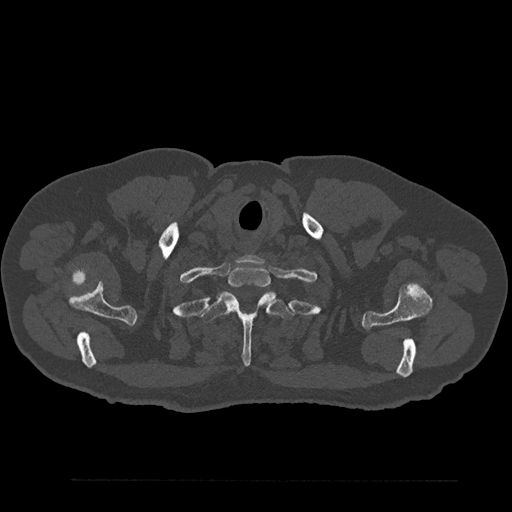
CT including the spine, one axial slice. Slice 735 of 797 in the series (ordered by position). Reconstruction kernel Br40s/3. Bone window (W 1800 / L 400 HU). 512 × 512 image matrix. Male patient, age 61 years. Case-level facts recorded for this patient, not image findings: primary cancer: prostate.
Structures marked on this image (semi-automatically segmented with operator editing):
- T1 vertebra: bounding box <228,265,271,287> (left, top, right, bottom; pixels)
- T2 vertebra: <201,292,294,366>